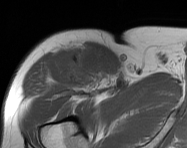
MRI of an extremity soft-tissue mass, one axial slice. Position 108 of 114 along the scan axis. MR volume resampled by the dataset authors to the PET/CT grid (not the native acquisition matrix). 187 × 148 image matrix, field of view 183 × 145 mm. Male patient. Case-level facts recorded for this patient, not image findings: histological type: pleiomorphic leiomyosarcoma; grade: intermediate; site of the primary tumour: right thigh.
Structures marked on this image (expert contour drawn on MRI and transferred to this co-registered scan by the dataset authors):
- gross tumour volume including surrounding oedema: box from (x=68, y=47) to (x=108, y=91) px
- gross tumour volume (mass): (x=75, y=56)–(x=106, y=87)